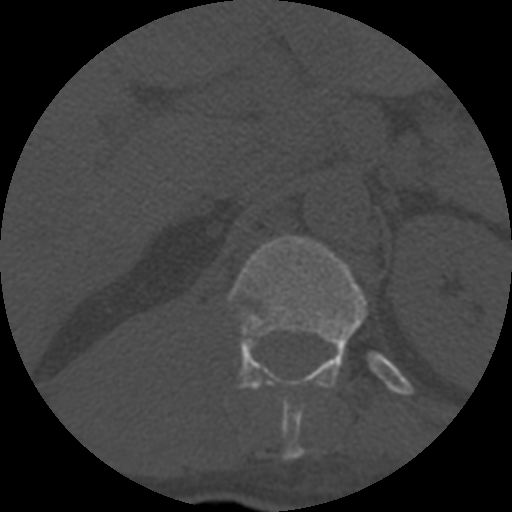
CT including the spine, one axial slice. Position 311 of 708 along the scan axis. Reconstruction kernel STANDARD. 120 kVp. One of 3 acquisitions stored at this slice position. Bone window (W 1800 / L 400 HU). 512 × 512 image matrix, field of view 160 × 160 mm. Patient age 55 years. Case-level facts recorded for this patient, not image findings: primary cancer: colon; vertebrae with lytic lesions (as recorded): T12, L1, L5.
Structures marked on this image (semi-automatically segmented with operator editing):
- T12 vertebra: bounding box <228,236,367,460> (left, top, right, bottom; pixels)